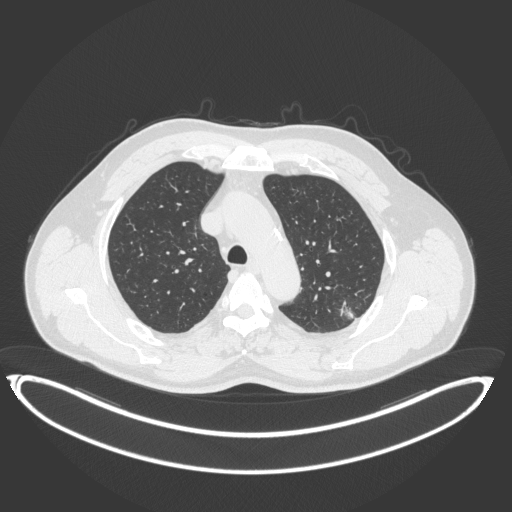
Chest CT, one axial slice. Position 272 of 399 along the scan axis. Lung window (W 1500 / L -600 HU). 512 × 512 image matrix. Patient: male, 58 years. Case-level facts recorded for this patient, not image findings: clinical TNM (as recorded): T1c N0 M0; histopathological grade: G1-2.
Structures marked on this image (bounding box drawn by a radiologist):
- lung tumour (recorded histology: adenocarcinoma): bounding box [x1, y1, x2, y2] px = [337, 302, 359, 320]